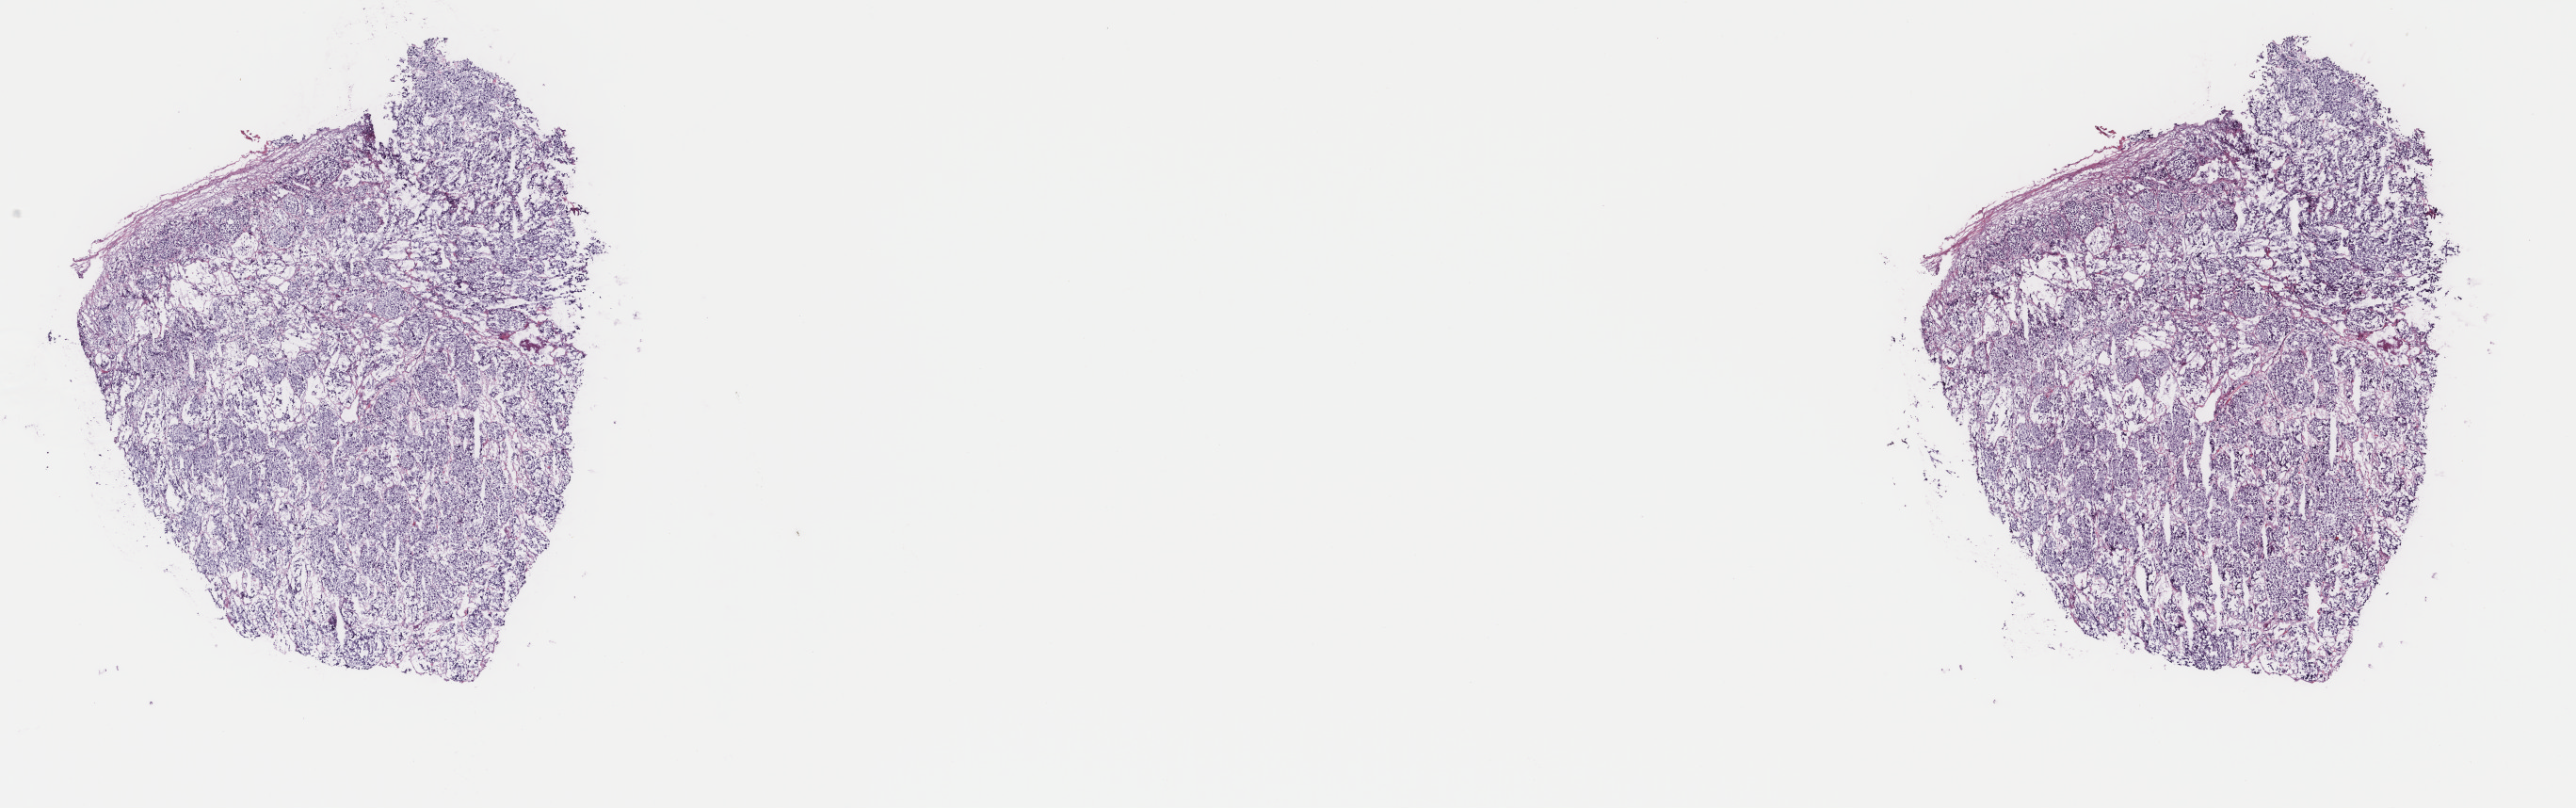
Digitized Hematoxylin and eosin (H&E) stained tissue section (whole slide) — shown as a low-resolution overview of the whole scanned area (about 21.7 x 6.8 mm, slide scanned at 40x); frozen section from the top of the tissue portion; primary tumour sample from the adrenal gland. Patient: female, age at initial diagnosis 30 years. Pathologist review of this section (percent, as recorded): tumour cells 100%, tumour nuclei 80%, normal cells 0%, stromal cells 0%, necrosis 0%. Infiltration values recorded for this section: lymphocyte infiltration 1%, monocyte infiltration 0%, neutrophil infiltration 0%.
Histologic diagnosis: Pheochromocytoma, NOS. Laterality: left.